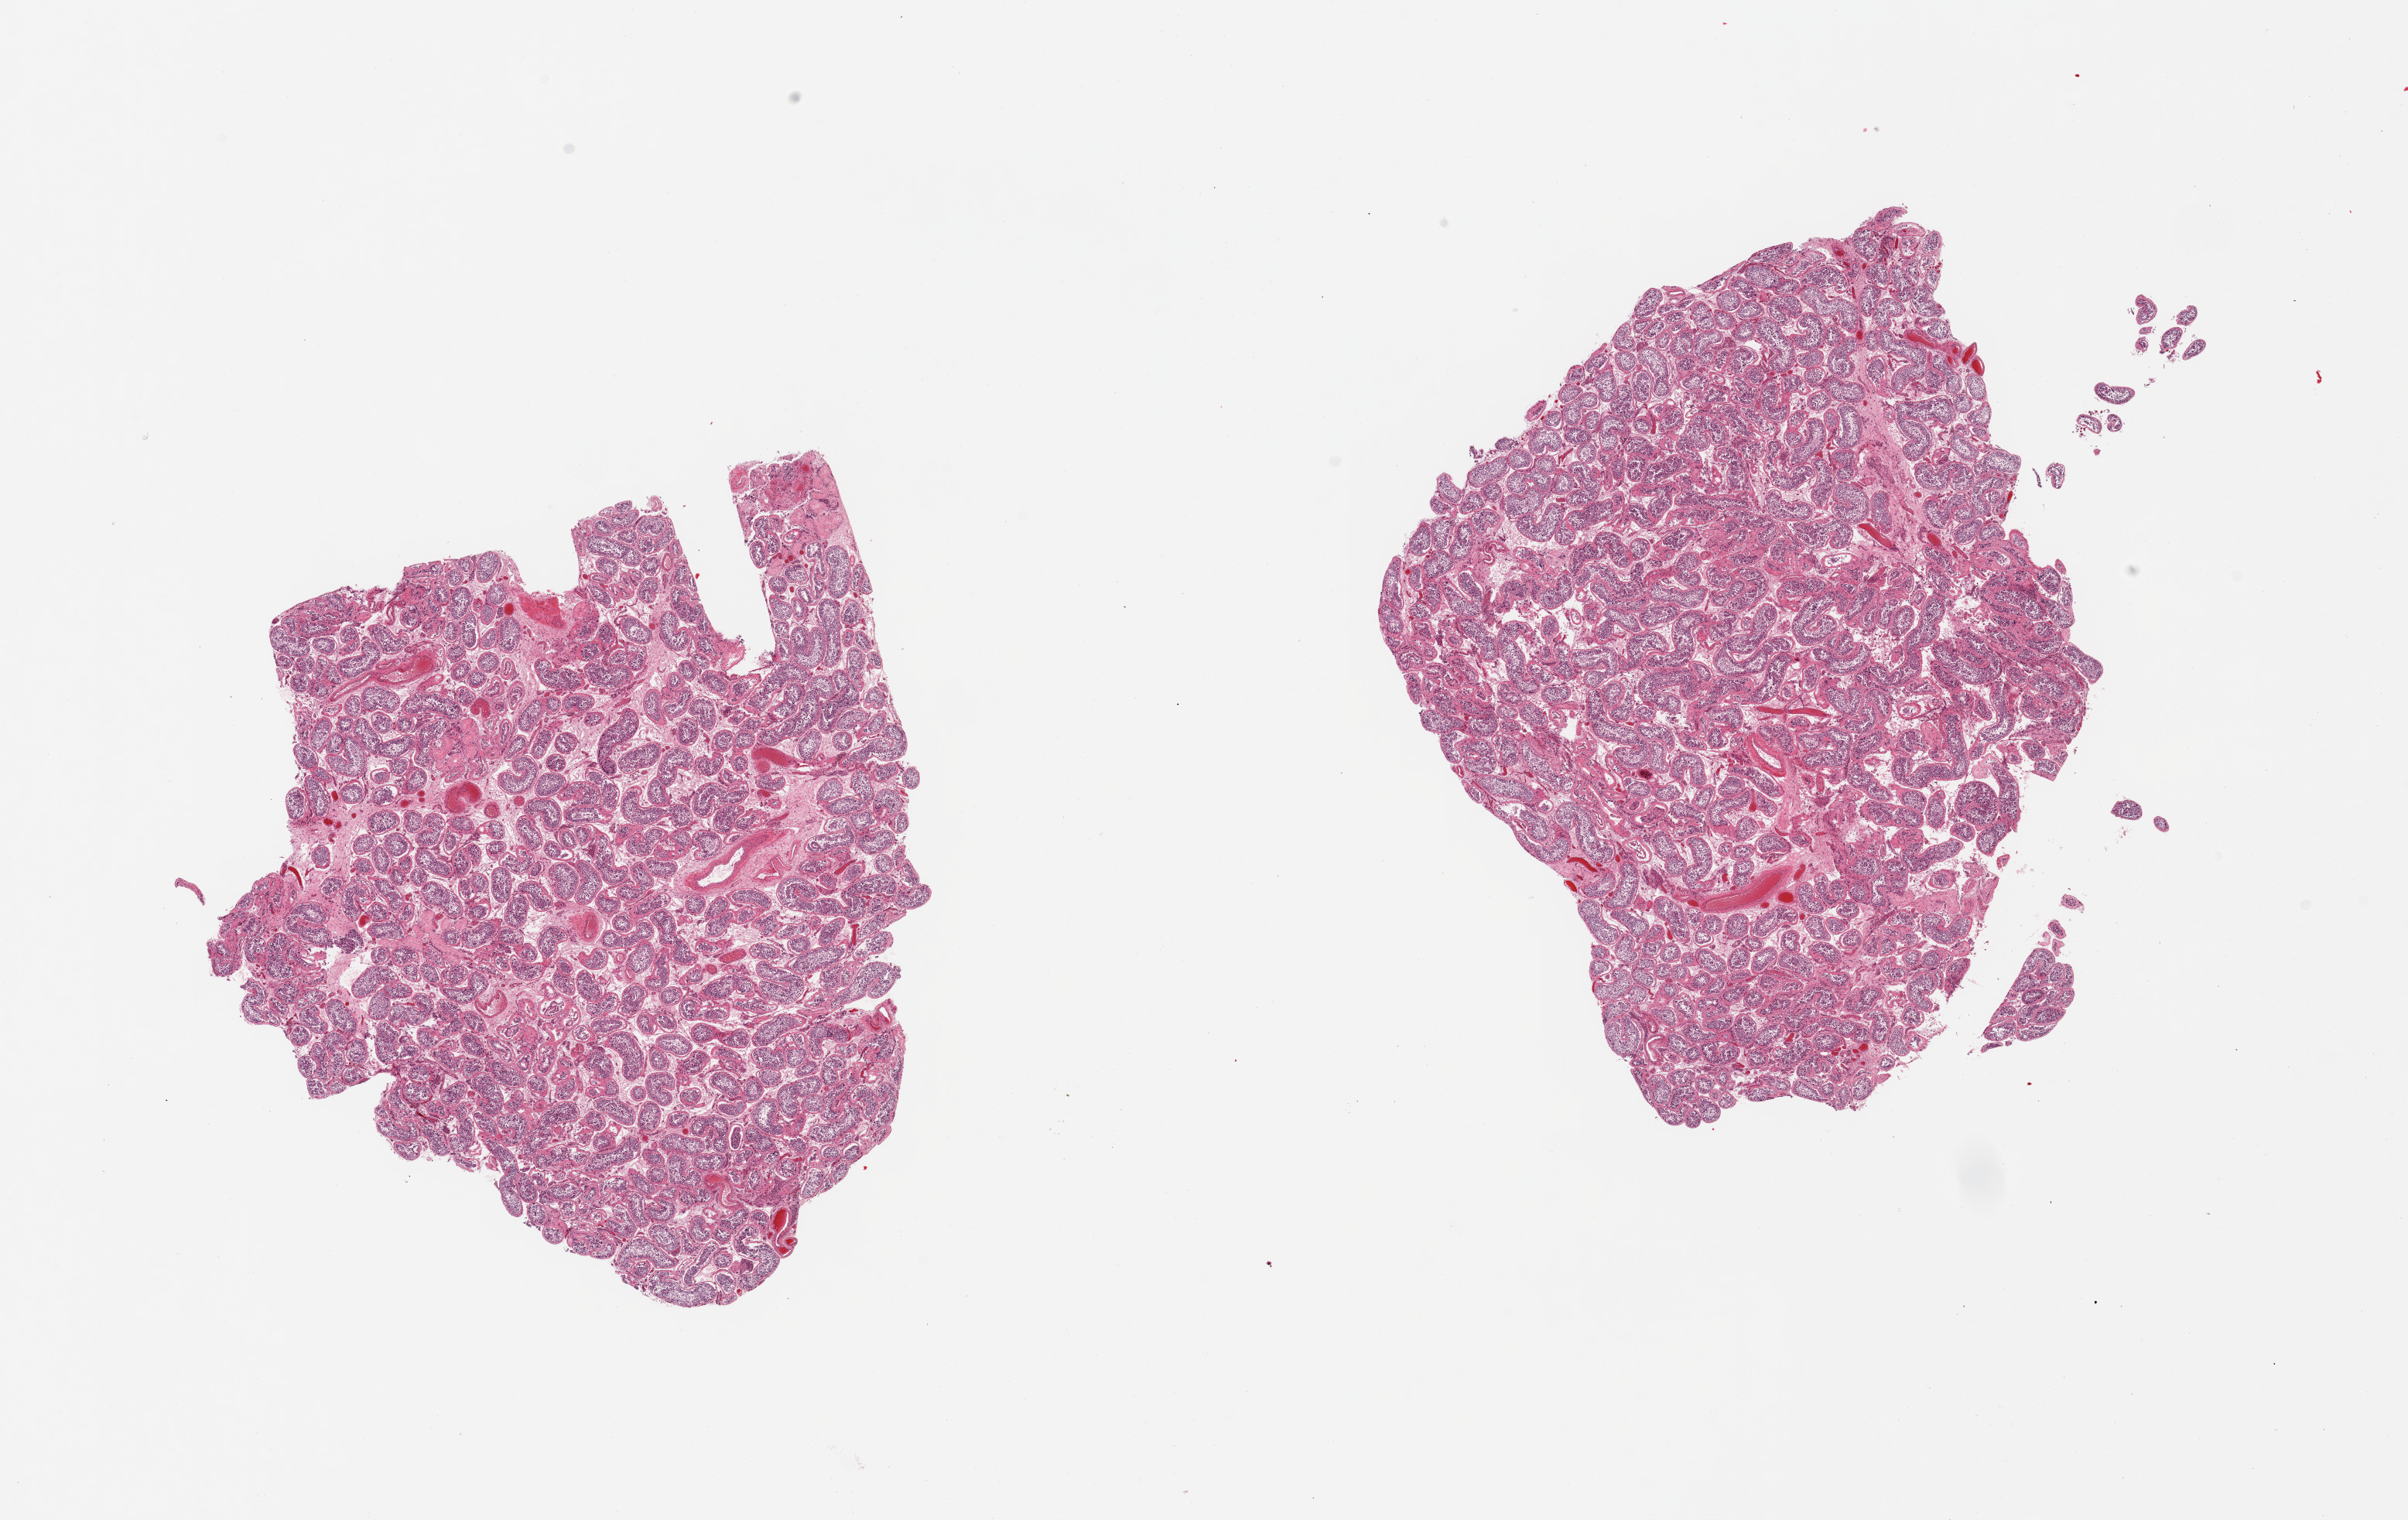
Whole-slide image, haematoxylin and eosin stain, low-resolution overview of the scanned area, about 24.6 x 15.5 mm (slide scanned at 20x); PAXgene-fixed, paraffin-embedded tissue; section of testis (target tissue); donor tissue sample. Donor: male.
Pathologist's review note for this sample: 2 pieces; spermatogenesis is present, some seminiferous tubules are hyalinized.